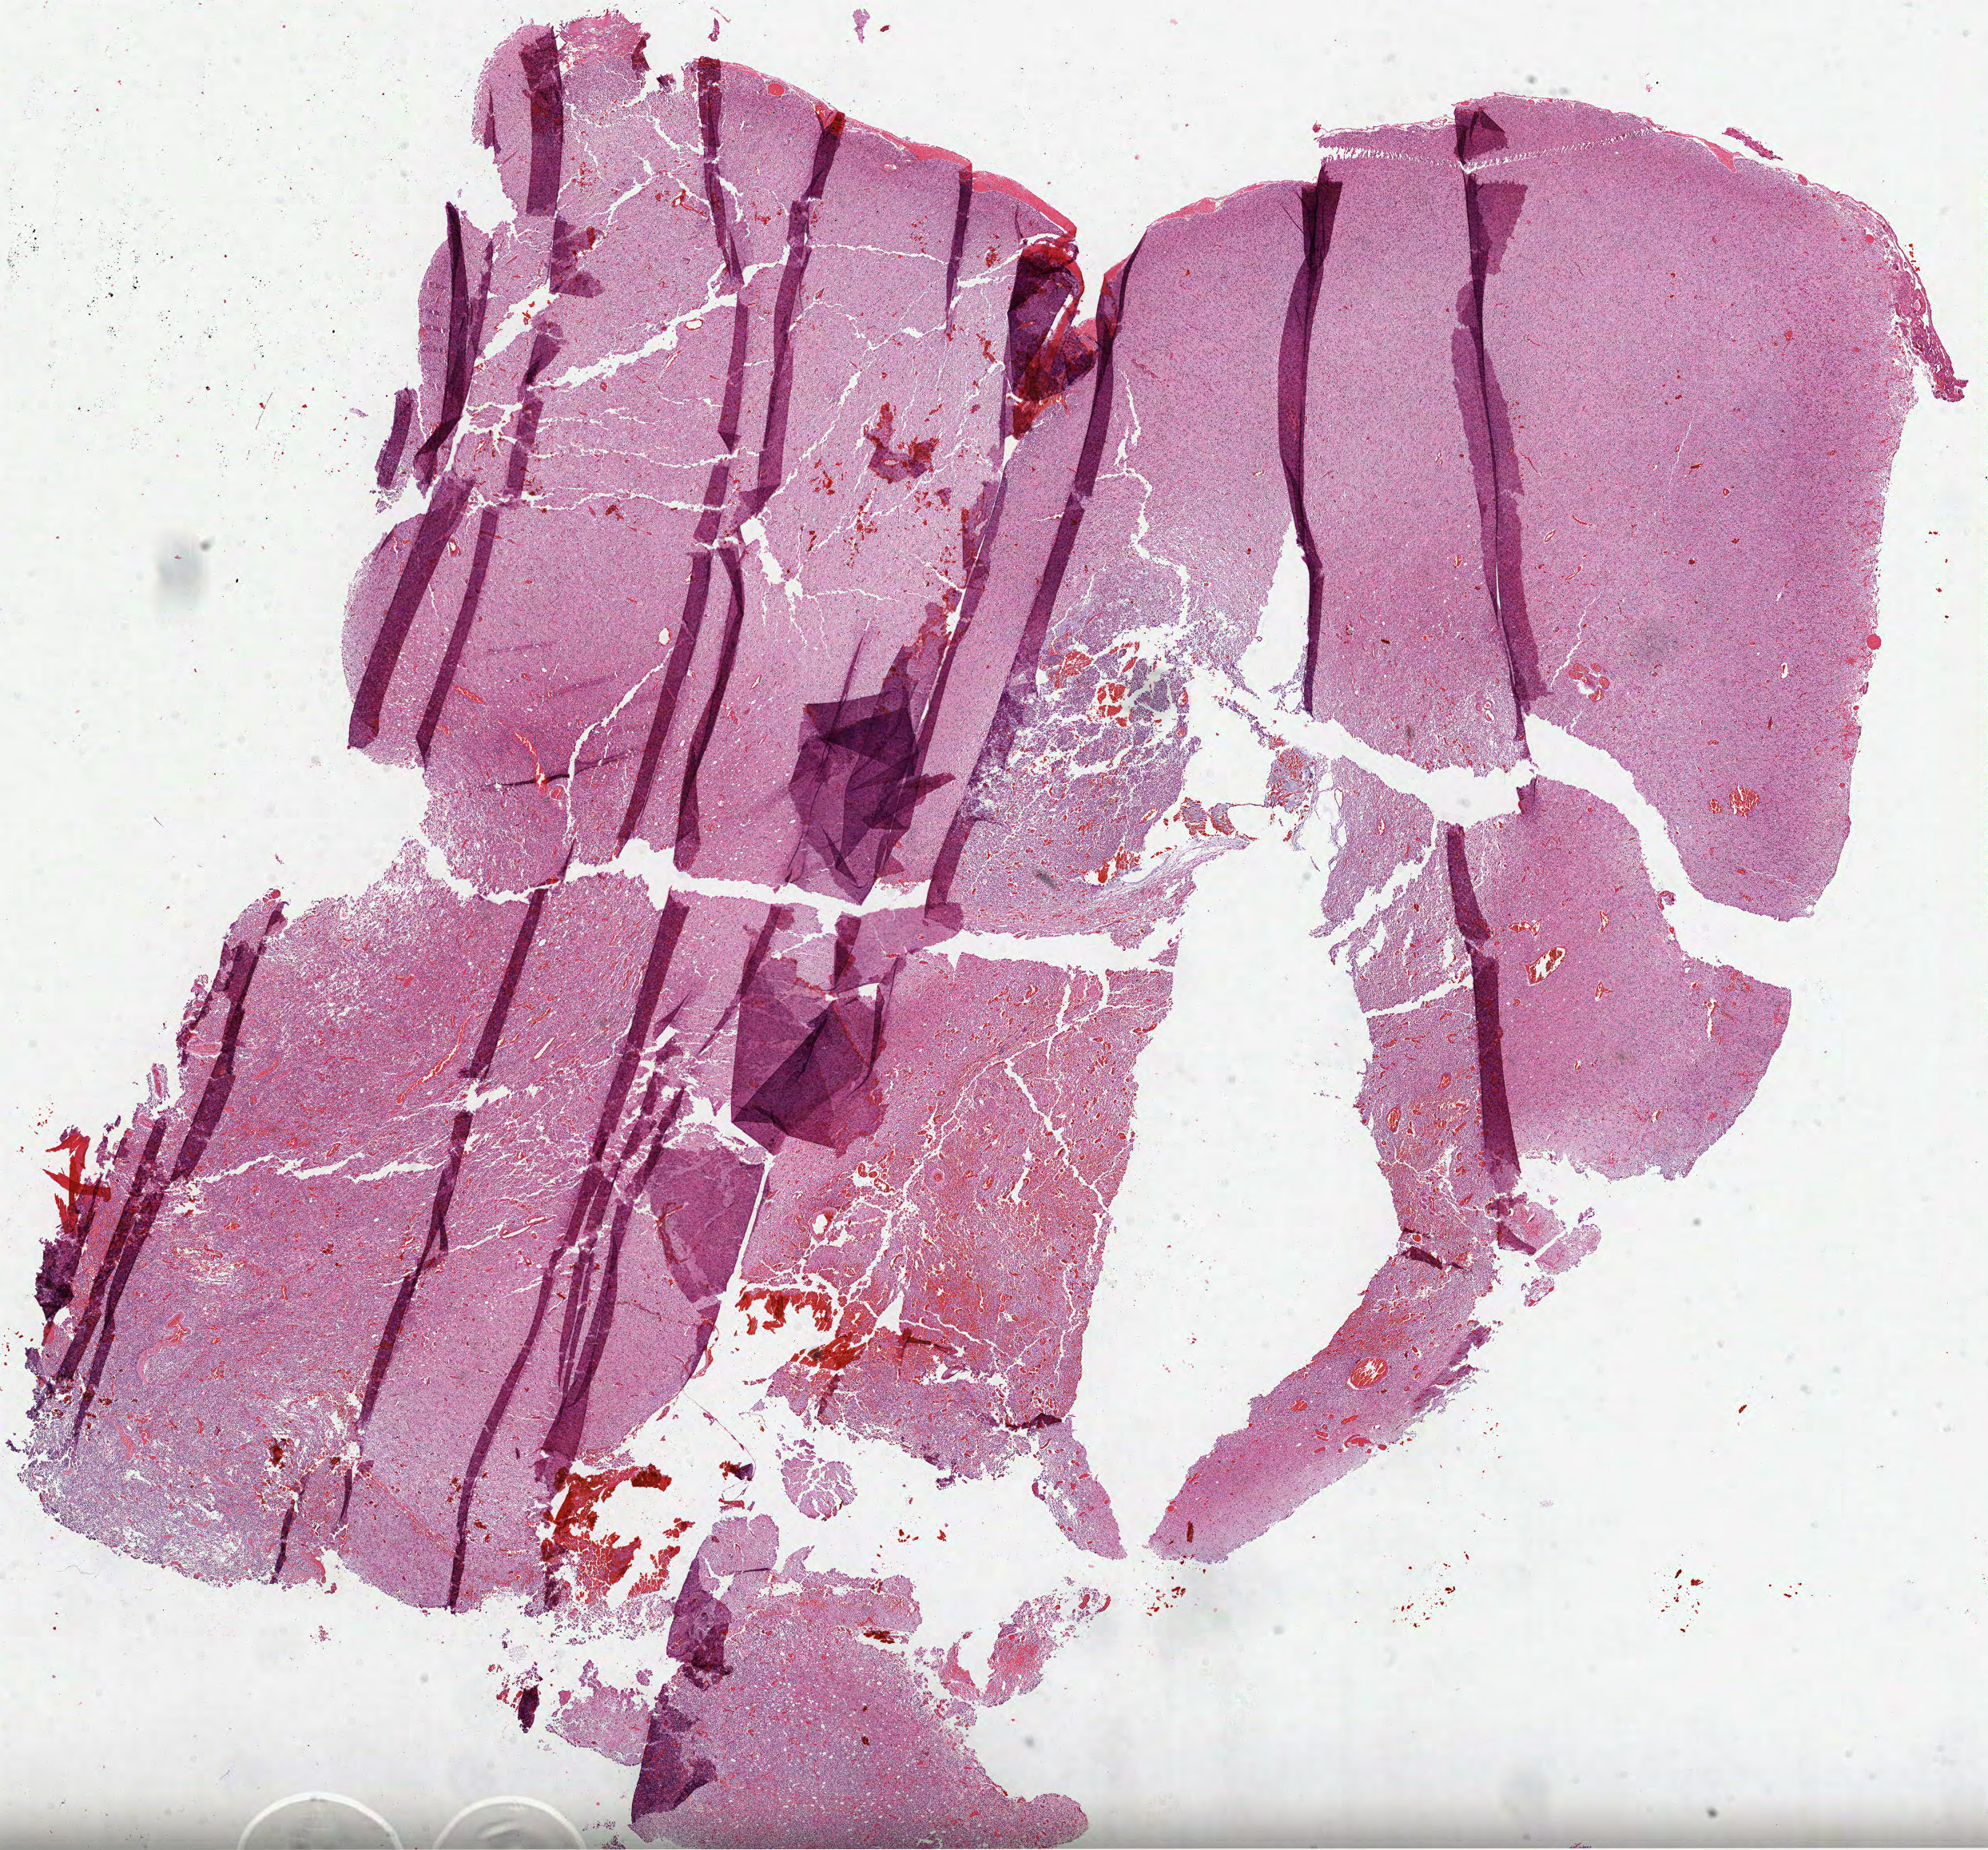
Hematoxylin and eosin (H&E) stained whole-slide image — shown as a low-resolution overview of the whole scanned area (about 20.1 x 18.7 mm). Formalin-fixed paraffin-embedded (FFPE) diagnostic section. Brain, primary tumour sample. Patient: male, age at initial diagnosis 39 years. Histologic grade: G2 (moderately differentiated).
Pathologic diagnosis: Oligodendroglioma, NOS. Laterality: left.